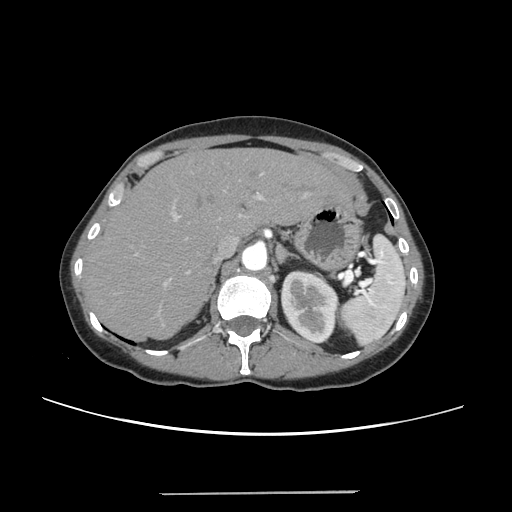
Contrast-enhanced abdominal CT, one axial slice; position 173 of 240 along the scan axis; 120 kVp; intravenous contrast given; soft-tissue window (W 400 / L 40 HU); 1.25 mm slice thickness; 512 × 512 image matrix, field of view 371 × 371 mm. Female patient, age 60 years. Case-level facts recorded for this patient, not image findings: diagnosis: colorectal cancer liver metastases, imaged before liver resection; multiple liver metastases: no; largest metastasis: 1.5 cm.
Structures marked on this image (expert manual segmentation):
- liver: bounding box <86,150,348,339> (left, top, right, bottom; pixels)
- planned liver remnant (the part of the liver to remain after resection): <86,150,349,339>
- portal vein (with intrahepatic branches): <135,172,307,286>